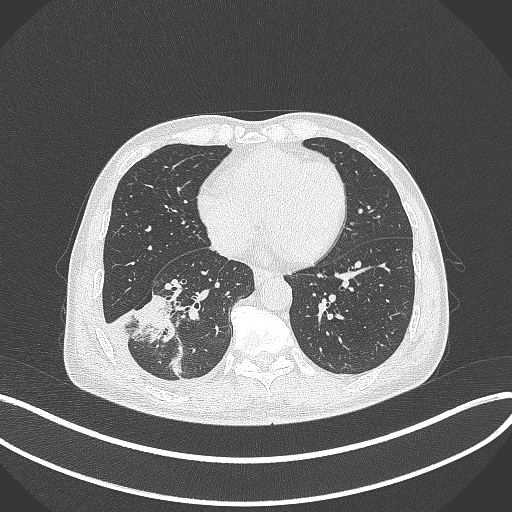
Chest CT, one axial slice. Position 137 of 388 along the scan axis. 120 kVp. Lung window (W 1500 / L -600 HU). 1 mm slice thickness. 512 × 512 image matrix. Patient: male, 64 years. Case-level facts recorded for this patient, not image findings: clinical TNM (as recorded): T3 N0 M0; histopathological grade: G2-3.
Structures marked on this image (bounding box drawn by a radiologist):
- lung tumour (recorded histology: adenocarcinoma): bounding box [x1, y1, x2, y2] px = [127, 288, 178, 352]